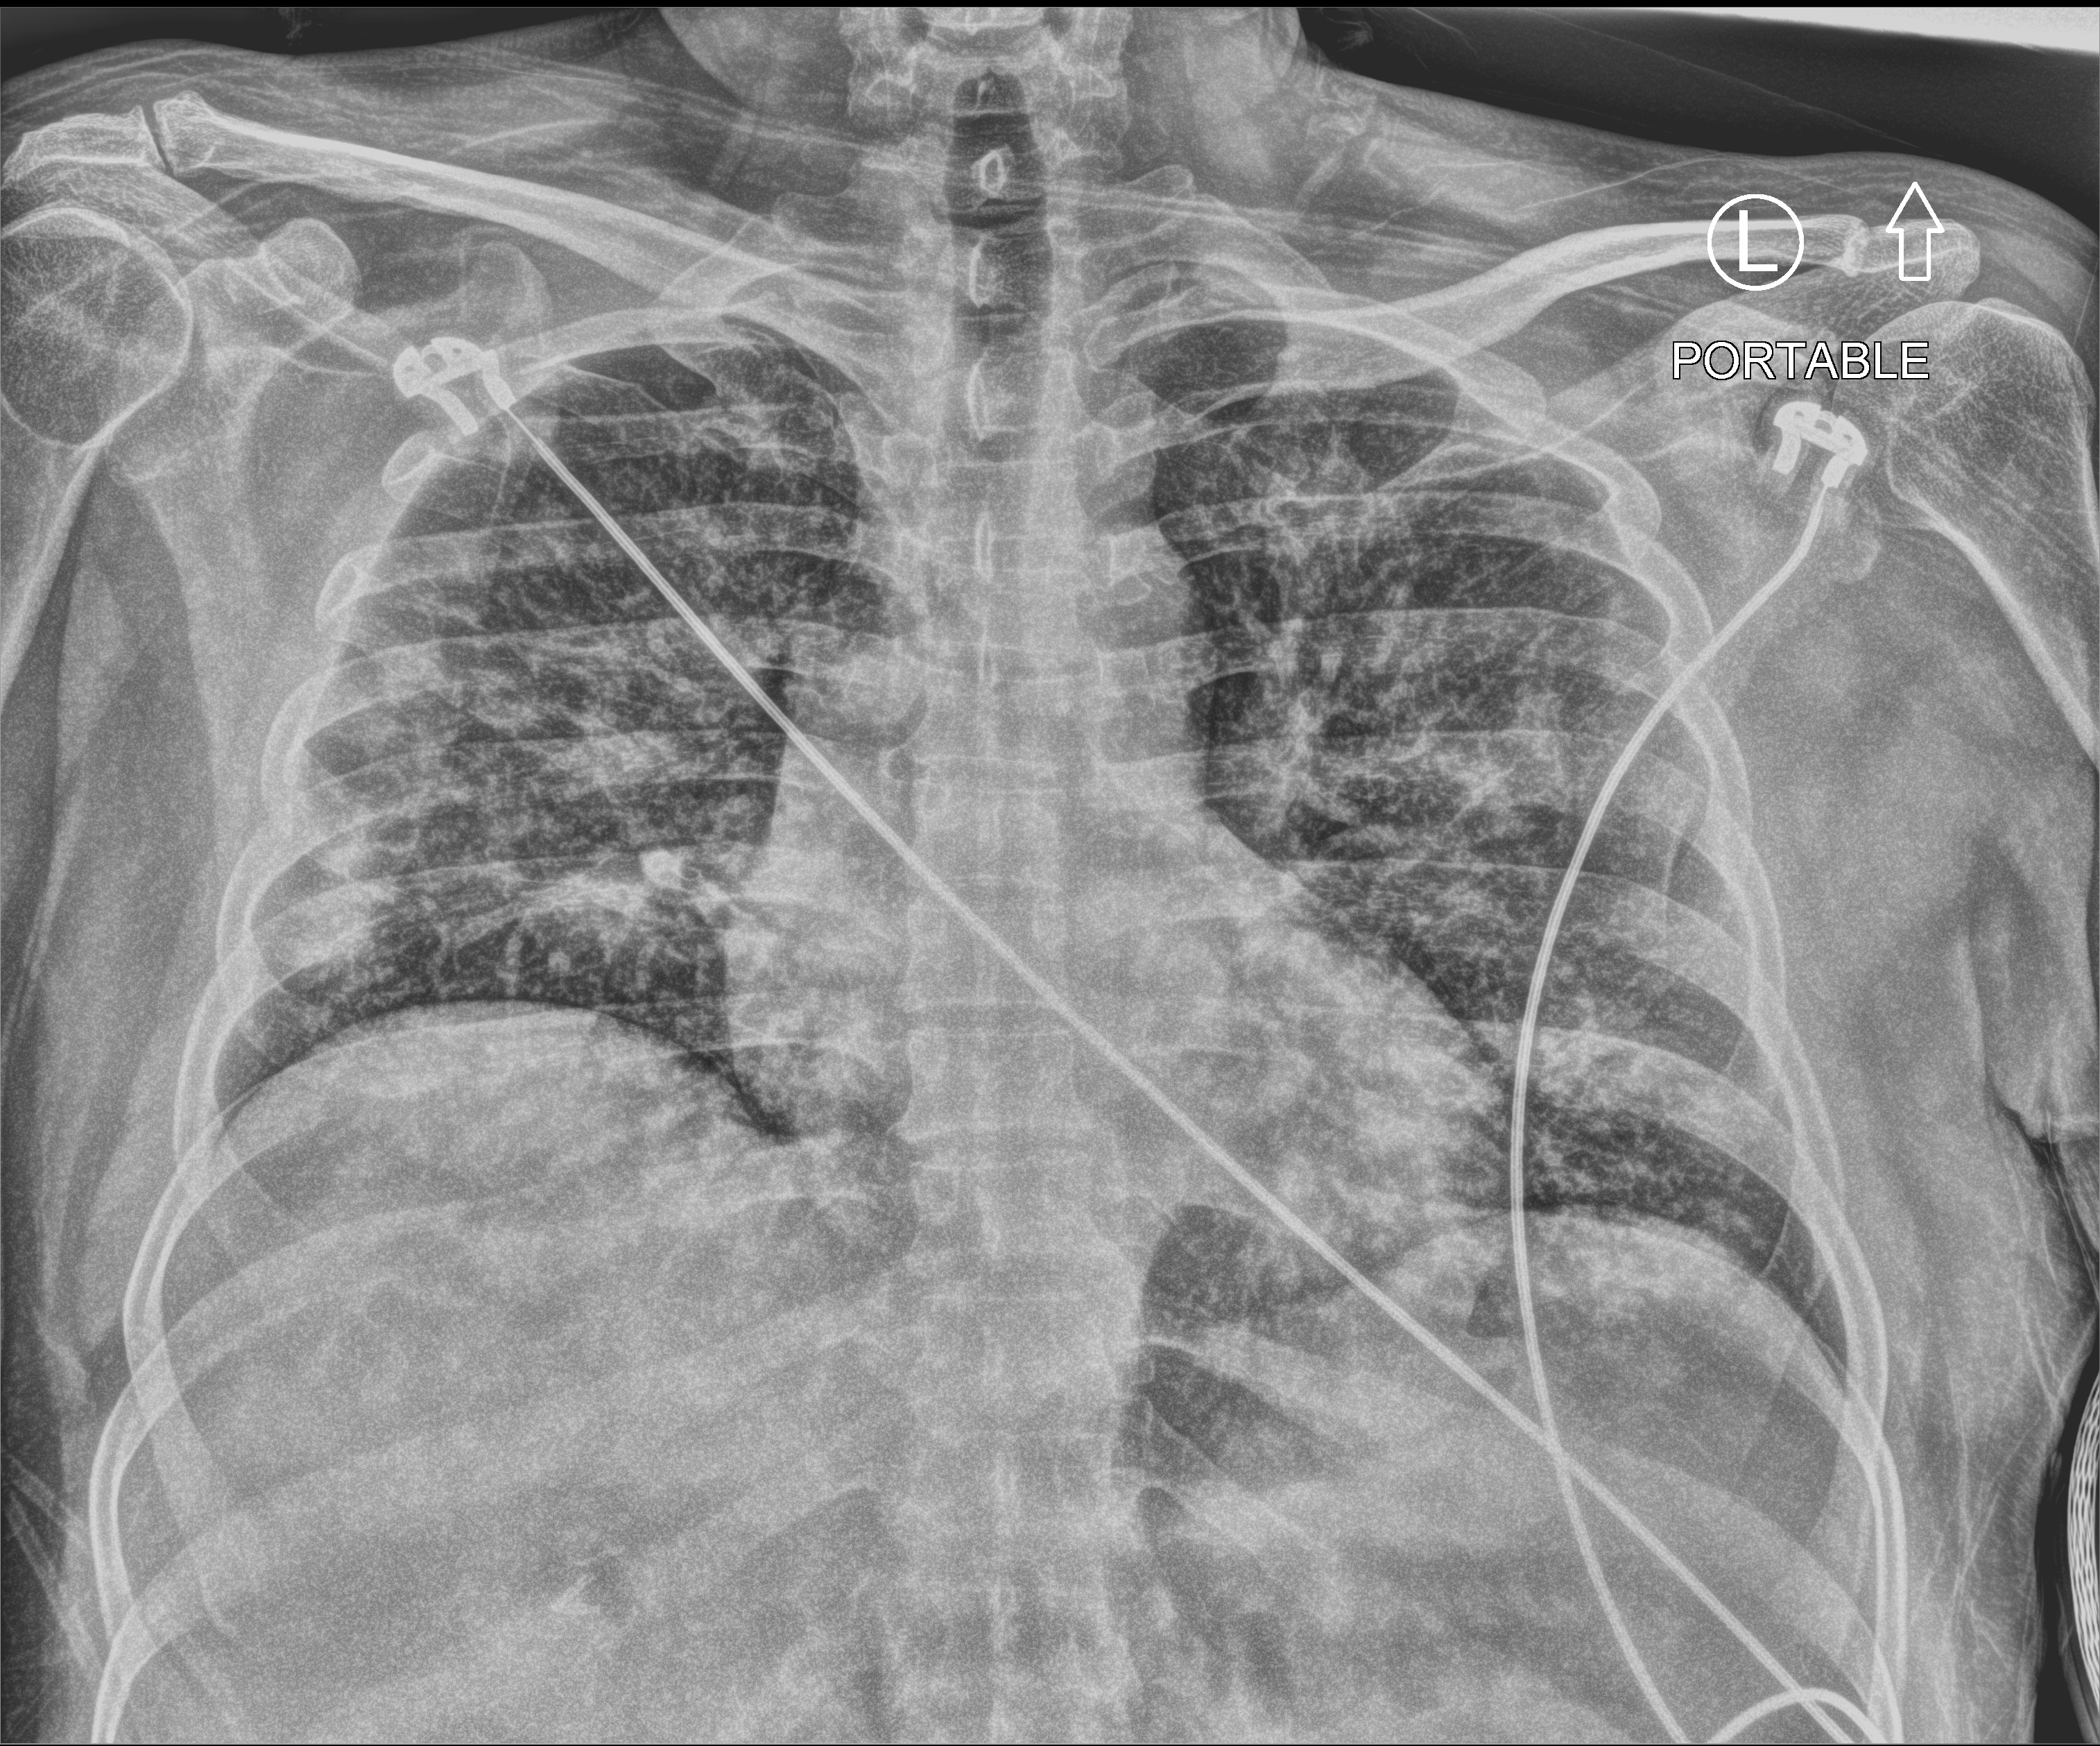
Bedside chest radiograph (computed radiography); anteroposterior (AP) projection. Male patient hospitalised with COVID-19, age 18–59 years.
From the hospital-stay record, not from the radiograph (when in the stay this image was taken is not recorded): length of hospital stay: 2 days; chronic kidney disease (admission record): no; hypertension (admission record): no.